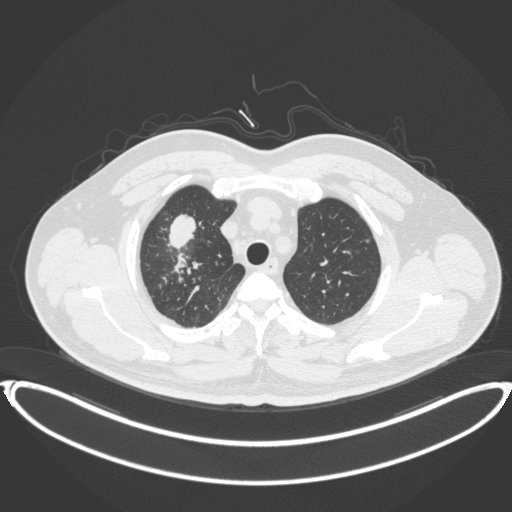
Chest CT, one axial slice; slice 316 of 399 in the series (ordered by position); 120 kVp; lung window (W 1500 / L -600 HU); 1 mm slice thickness; 512 × 512 image matrix, field of view 445 × 445 mm. Male patient, age 53 years. Case-level facts recorded for this patient, not image findings: clinical TNM (as recorded): T2a N0 M0.
Outlined on this slice (rectangle marked by the reading radiologist):
- lung tumour (recorded histology: adenocarcinoma): bounding box (x1, y1, x2, y2) in pixels: (165, 208, 200, 255)